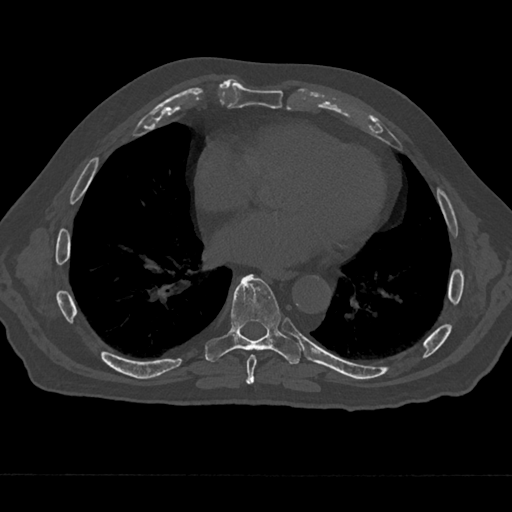
CT including the spine, one axial slice. Position 328 of 797 along the scan axis. Reconstruction kernel Br40s/3. Bone window (W 1800 / L 400 HU). 0.5 mm slice thickness. 512 × 512 image matrix, field of view 377 × 377 mm. Patient: male, 75 years. Case-level facts recorded for this patient, not image findings: primary cancer: renal.
Outlined on this slice (semi-automatically segmented with operator editing):
- T7 vertebra: bounding box (x1, y1, x2, y2) in pixels: (241, 354, 257, 385)
- T8 vertebra: (204, 274, 301, 364)